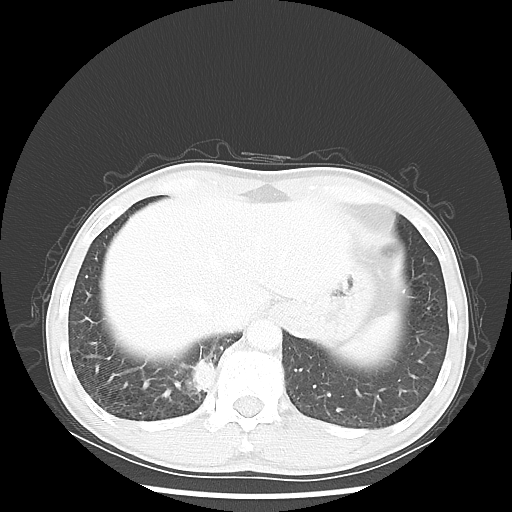
Chest CT, one axial slice; position 7 of 58 along the scan axis; reconstruction kernel LUNG; 100 kVp; lung window (W 1500 / L -600 HU); 5 mm slice thickness; 512 × 512 image matrix, field of view 360 × 360 mm. Male patient, age 56 years. From the clinical record (not read from this slice): clinical TNM (as recorded): T2 N1 M1.
Outlined on this slice (bounding box drawn by a radiologist):
- lung tumour (recorded histology: adenocarcinoma): box from (x=187, y=356) to (x=216, y=400) px